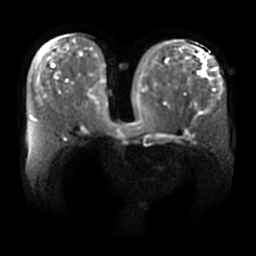
Breast MRI, one axial slice. Position 17 of 36 along the scan axis. Diffusion-weighted series; image 2 of 4 stored at this slice position (different b-values; order by instance number). 3 T. 256 × 256 image matrix. Female patient.
Structures marked on this image (expert manual segmentation):
- tumour on diffusion-weighted imaging: bounding box (x1, y1, x2, y2) in pixels: (198, 71, 205, 77)